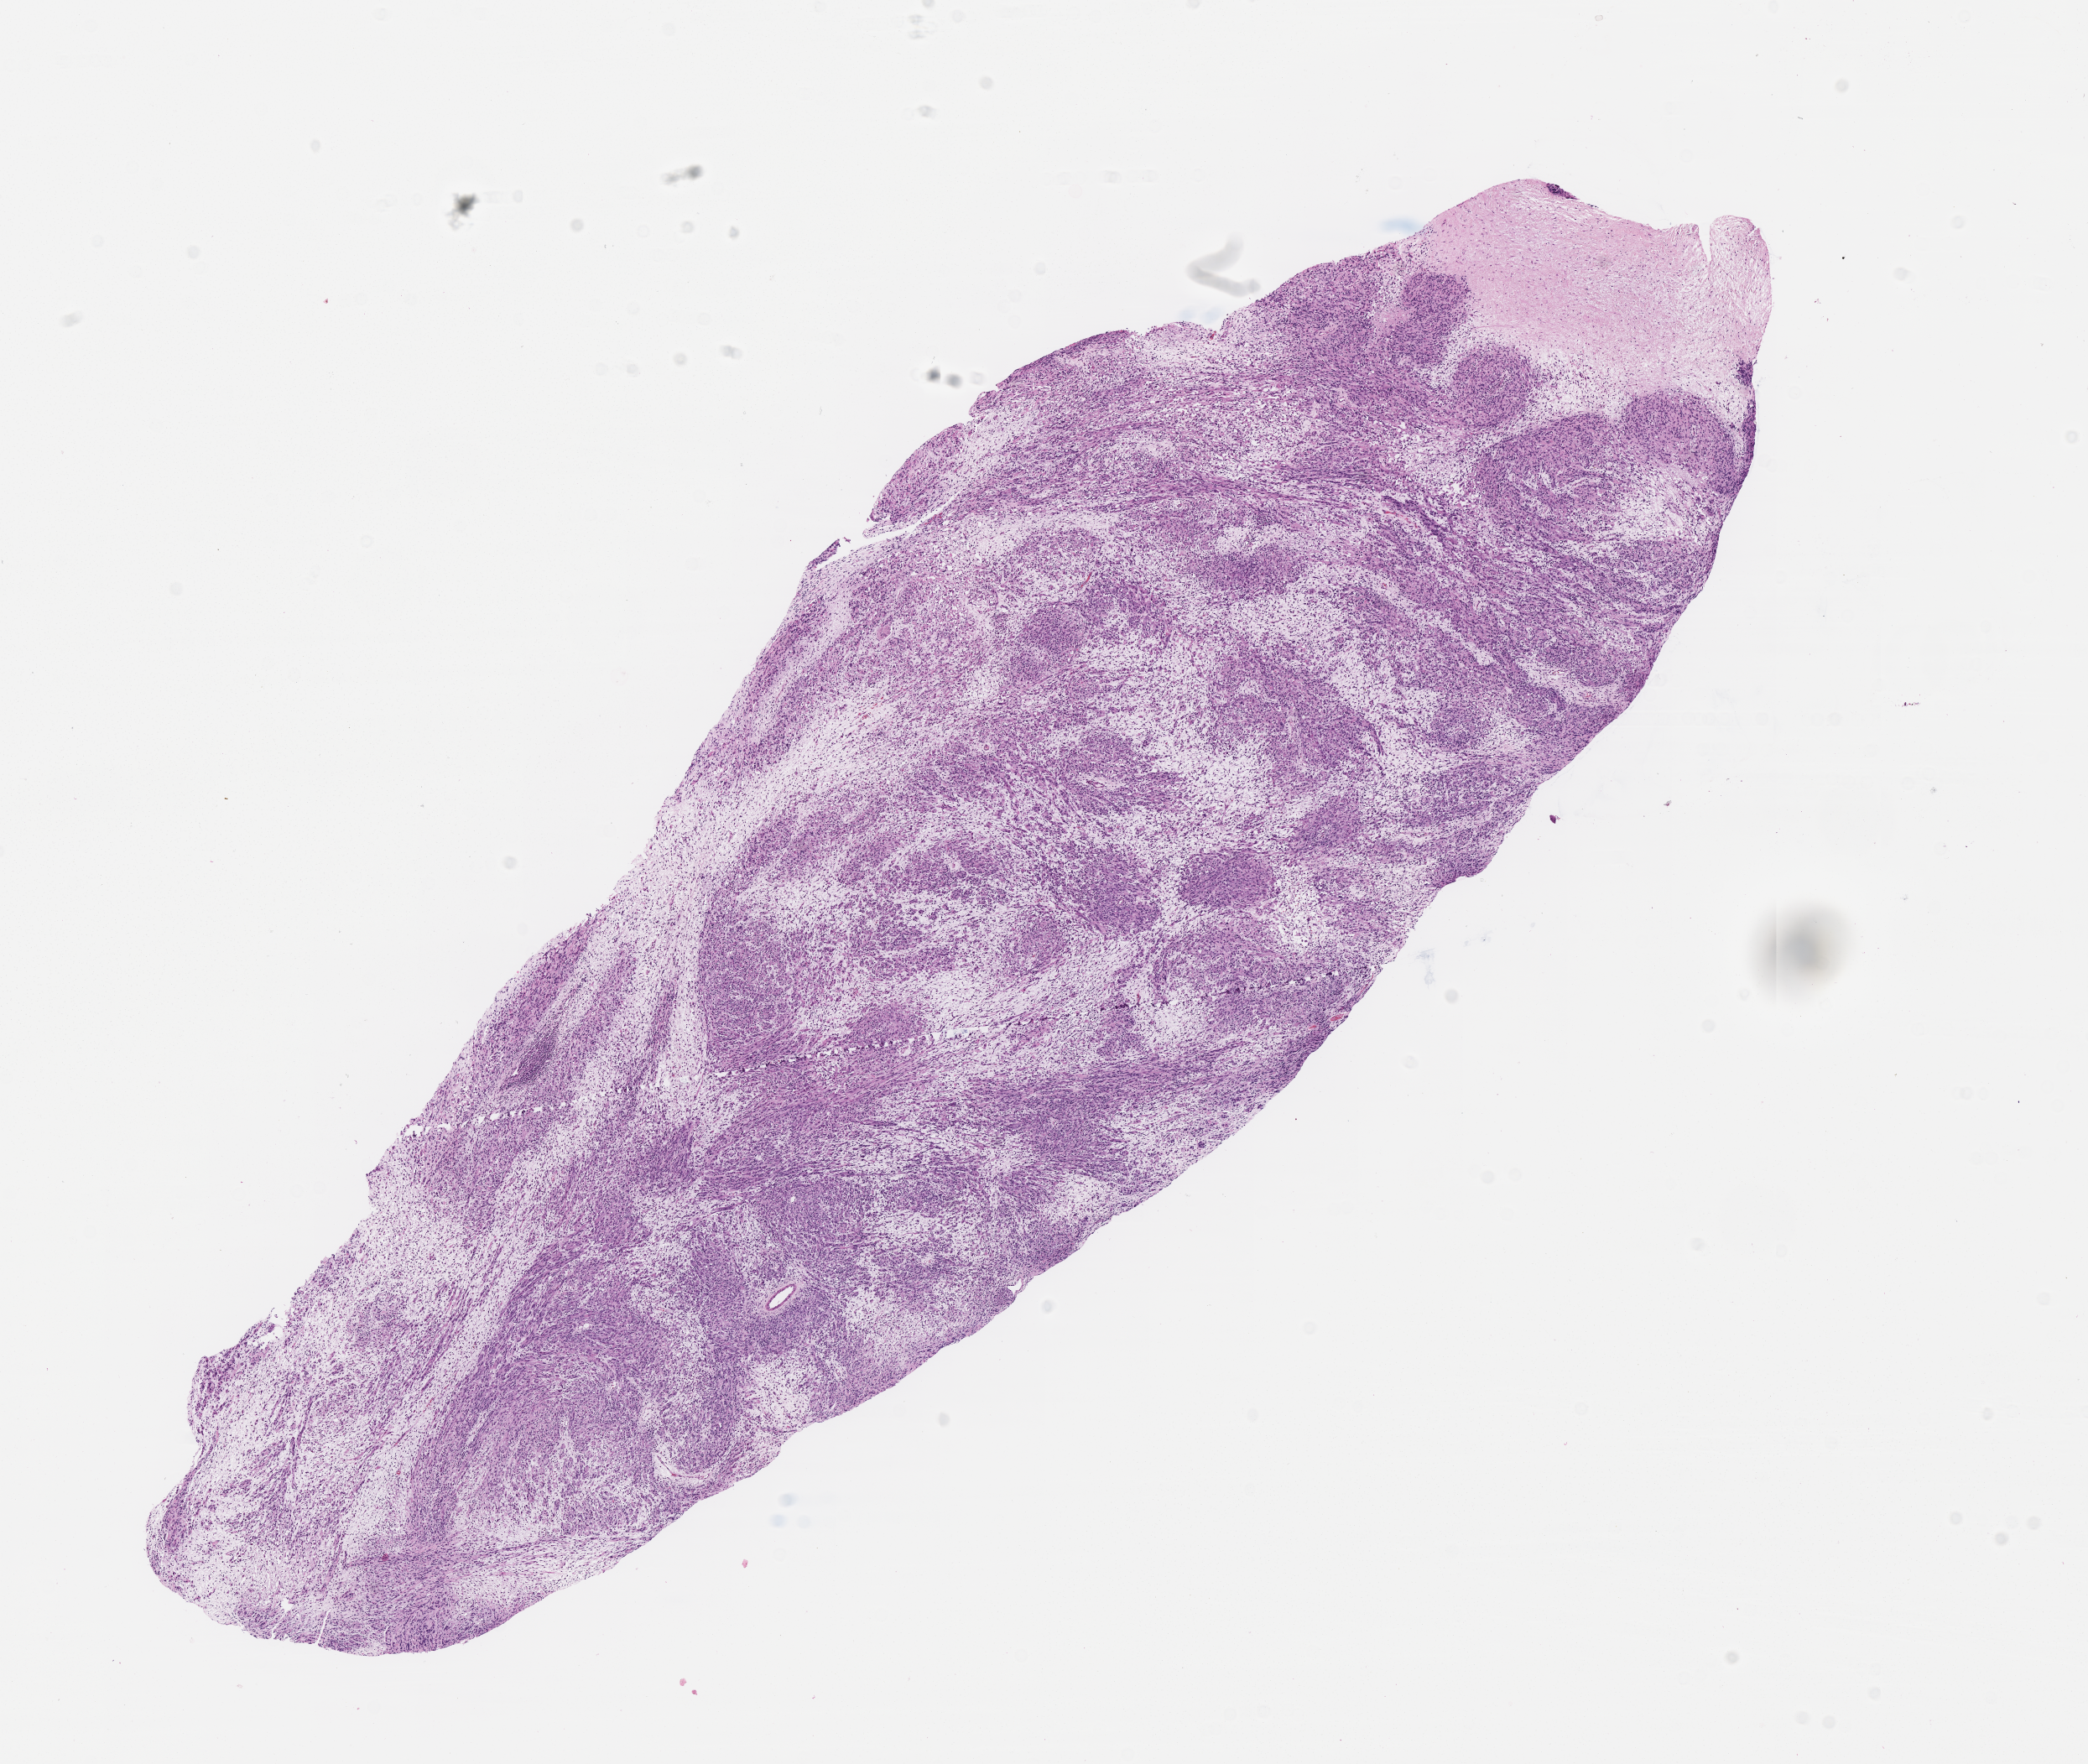
Digitized hematoxylin and eosin (H&E)-stained section of tumor tissue, whole scanned area (about 10.1 x 8.5 mm) shown as a low-resolution overview. FFPE section. Site: pelvis. Patient: male, age 0.5 years at diagnosis.
Diagnosis: rhabdomyosarcoma; histological classification: embryonal rhabdomyosarcoma. Stage (as recorded): 3. Metastatic status at presentation (as recorded): non-metastatic (confirmed).